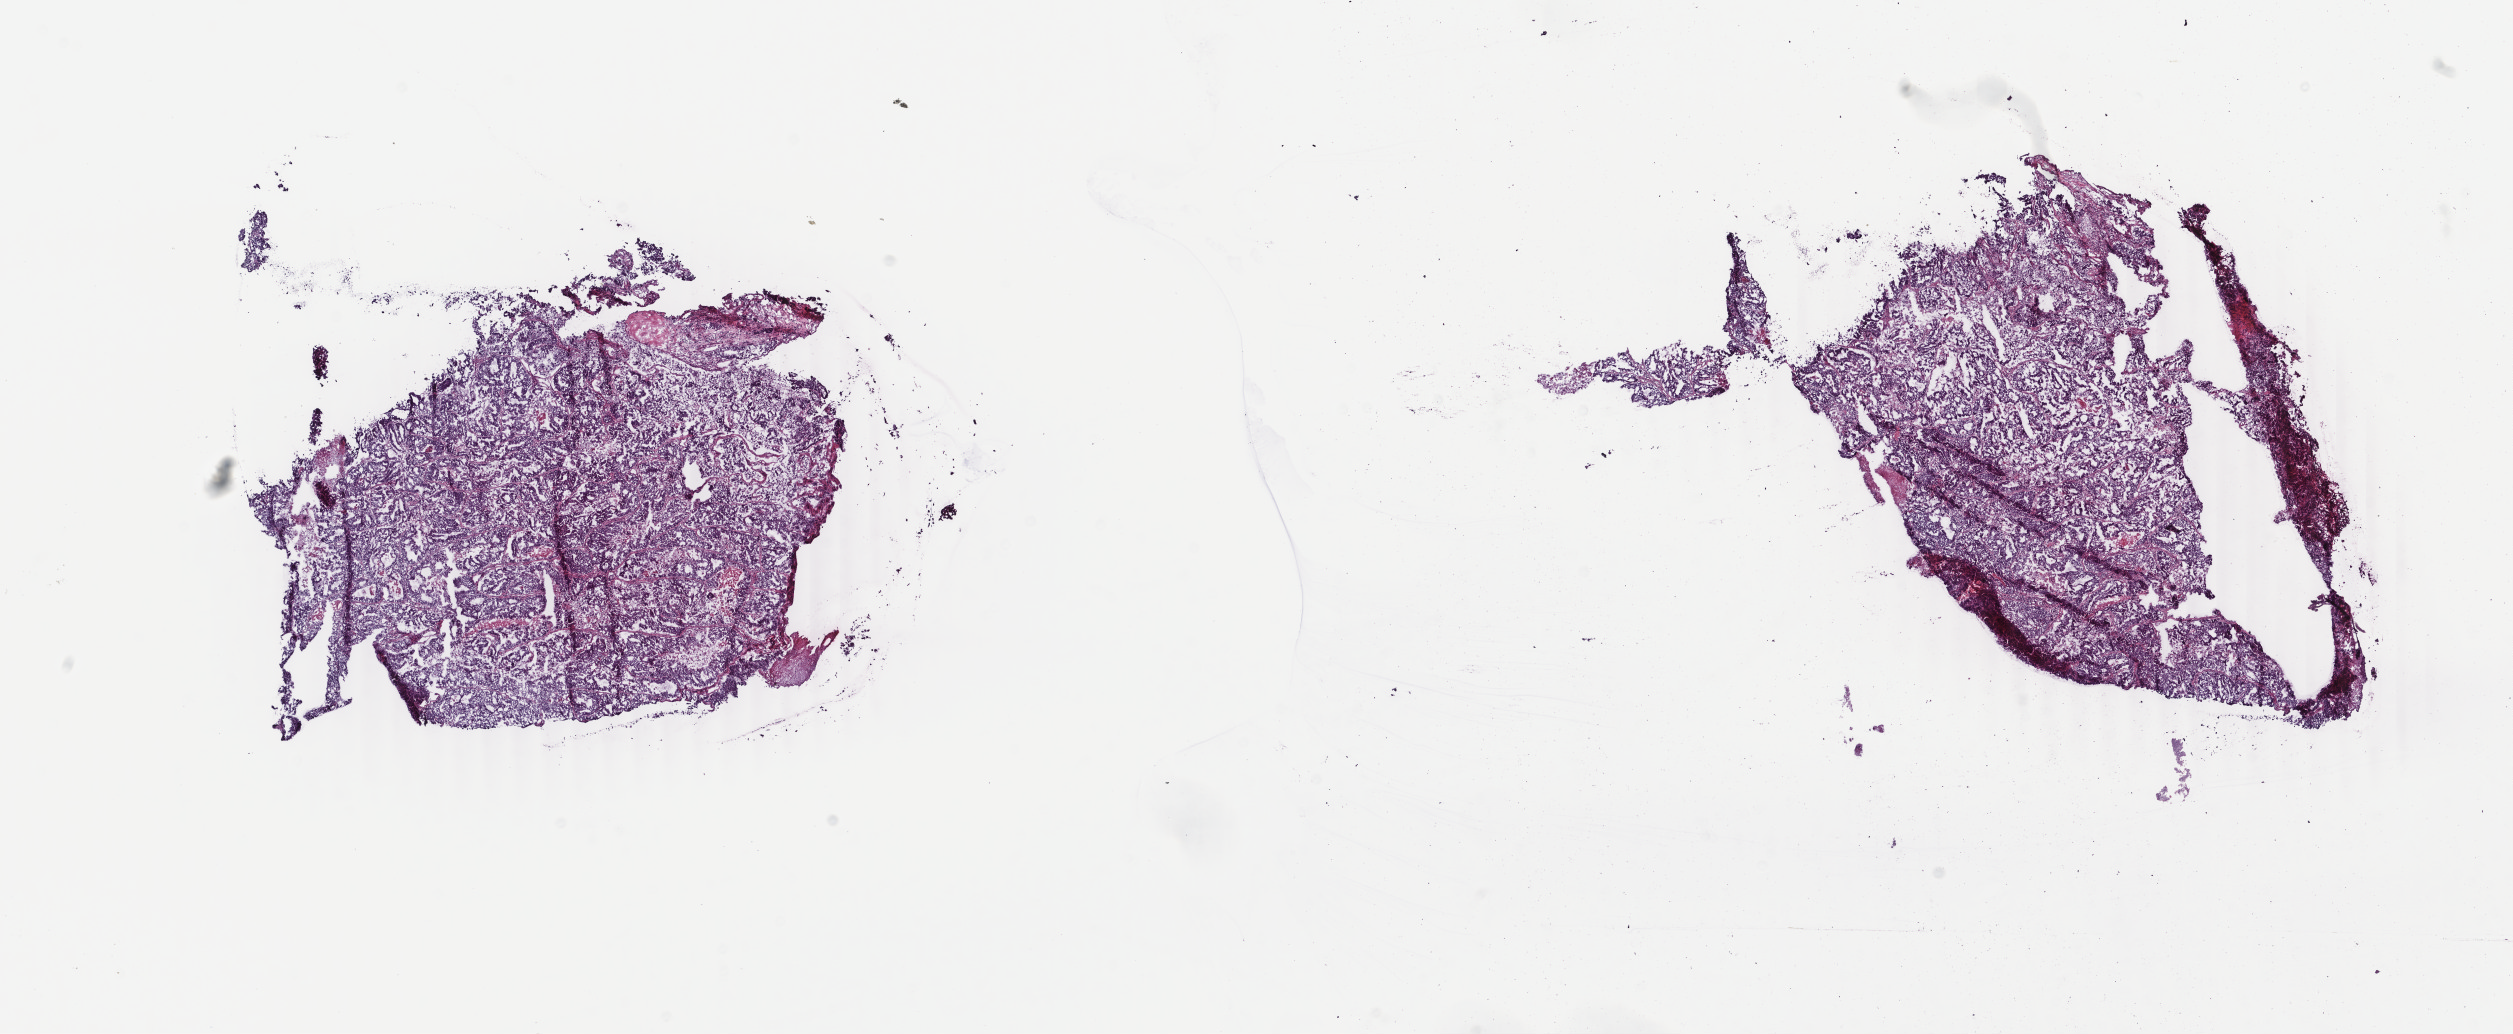
H&E whole-slide image — shown as a low-resolution overview of the whole scanned area (about 20.0 x 8.2 mm, slide scanned at 40x); frozen section from the top of the tissue portion; primary tumour sample from the uterus. Female patient; age at initial diagnosis 74 years.
Pathologic diagnosis: Endometrioid adenocarcinoma, NOS (endometrium).